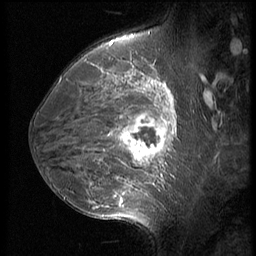
Breast MRI (dynamic contrast-enhanced), one sagittal slice; slice 38 of 56 in the series (ordered by position); 3 images stored at this slice position (order not interpretable as contrast timing); 1.5 T; TE 4.2 ms, TR 9 ms; 2.5 mm slice thickness; 256 × 256 image matrix. Patient: female, 35 years. Case-level facts recorded for this patient, not image findings: setting: breast cancer imaged before/during neoadjuvant chemotherapy; receptor status: HR-positive, HER2-negative.
Annotated regions visible in this slice (semi-automatic segmentation, software-assisted and operator-edited):
- analysis volume of interest (the breast-tissue region the enhancement analysis was run in; not a lesion): box from (x=63, y=60) to (x=190, y=218) px
- tumour enhancement mask (voxels above the 140 % enhancement threshold inside the analysis volume of interest): (x=105, y=83)–(x=174, y=208)